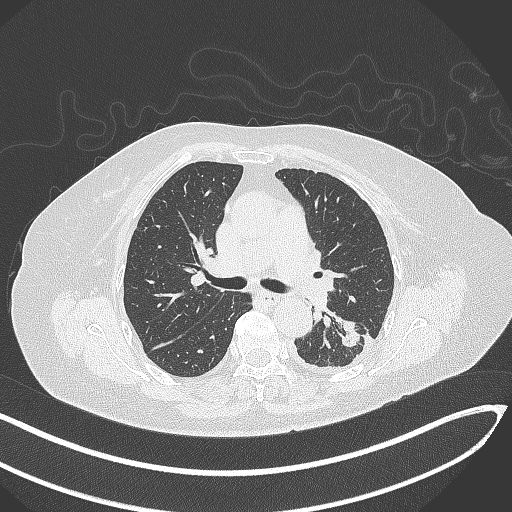
Chest CT, one axial slice. Slice 195 of 270 in the series (ordered by position). 120 kVp. Lung window (W 1500 / L -600 HU). 1 mm slice thickness. 512 × 512 image matrix, field of view 400 × 400 mm. Patient: female, 76 years. Case-level facts recorded for this patient, not image findings: clinical TNM (as recorded): T1c N0 M0.
Structures marked on this image (bounding box drawn by a radiologist):
- lung tumour (recorded histology: adenocarcinoma): bounding box <335,312,366,350> (left, top, right, bottom; pixels)